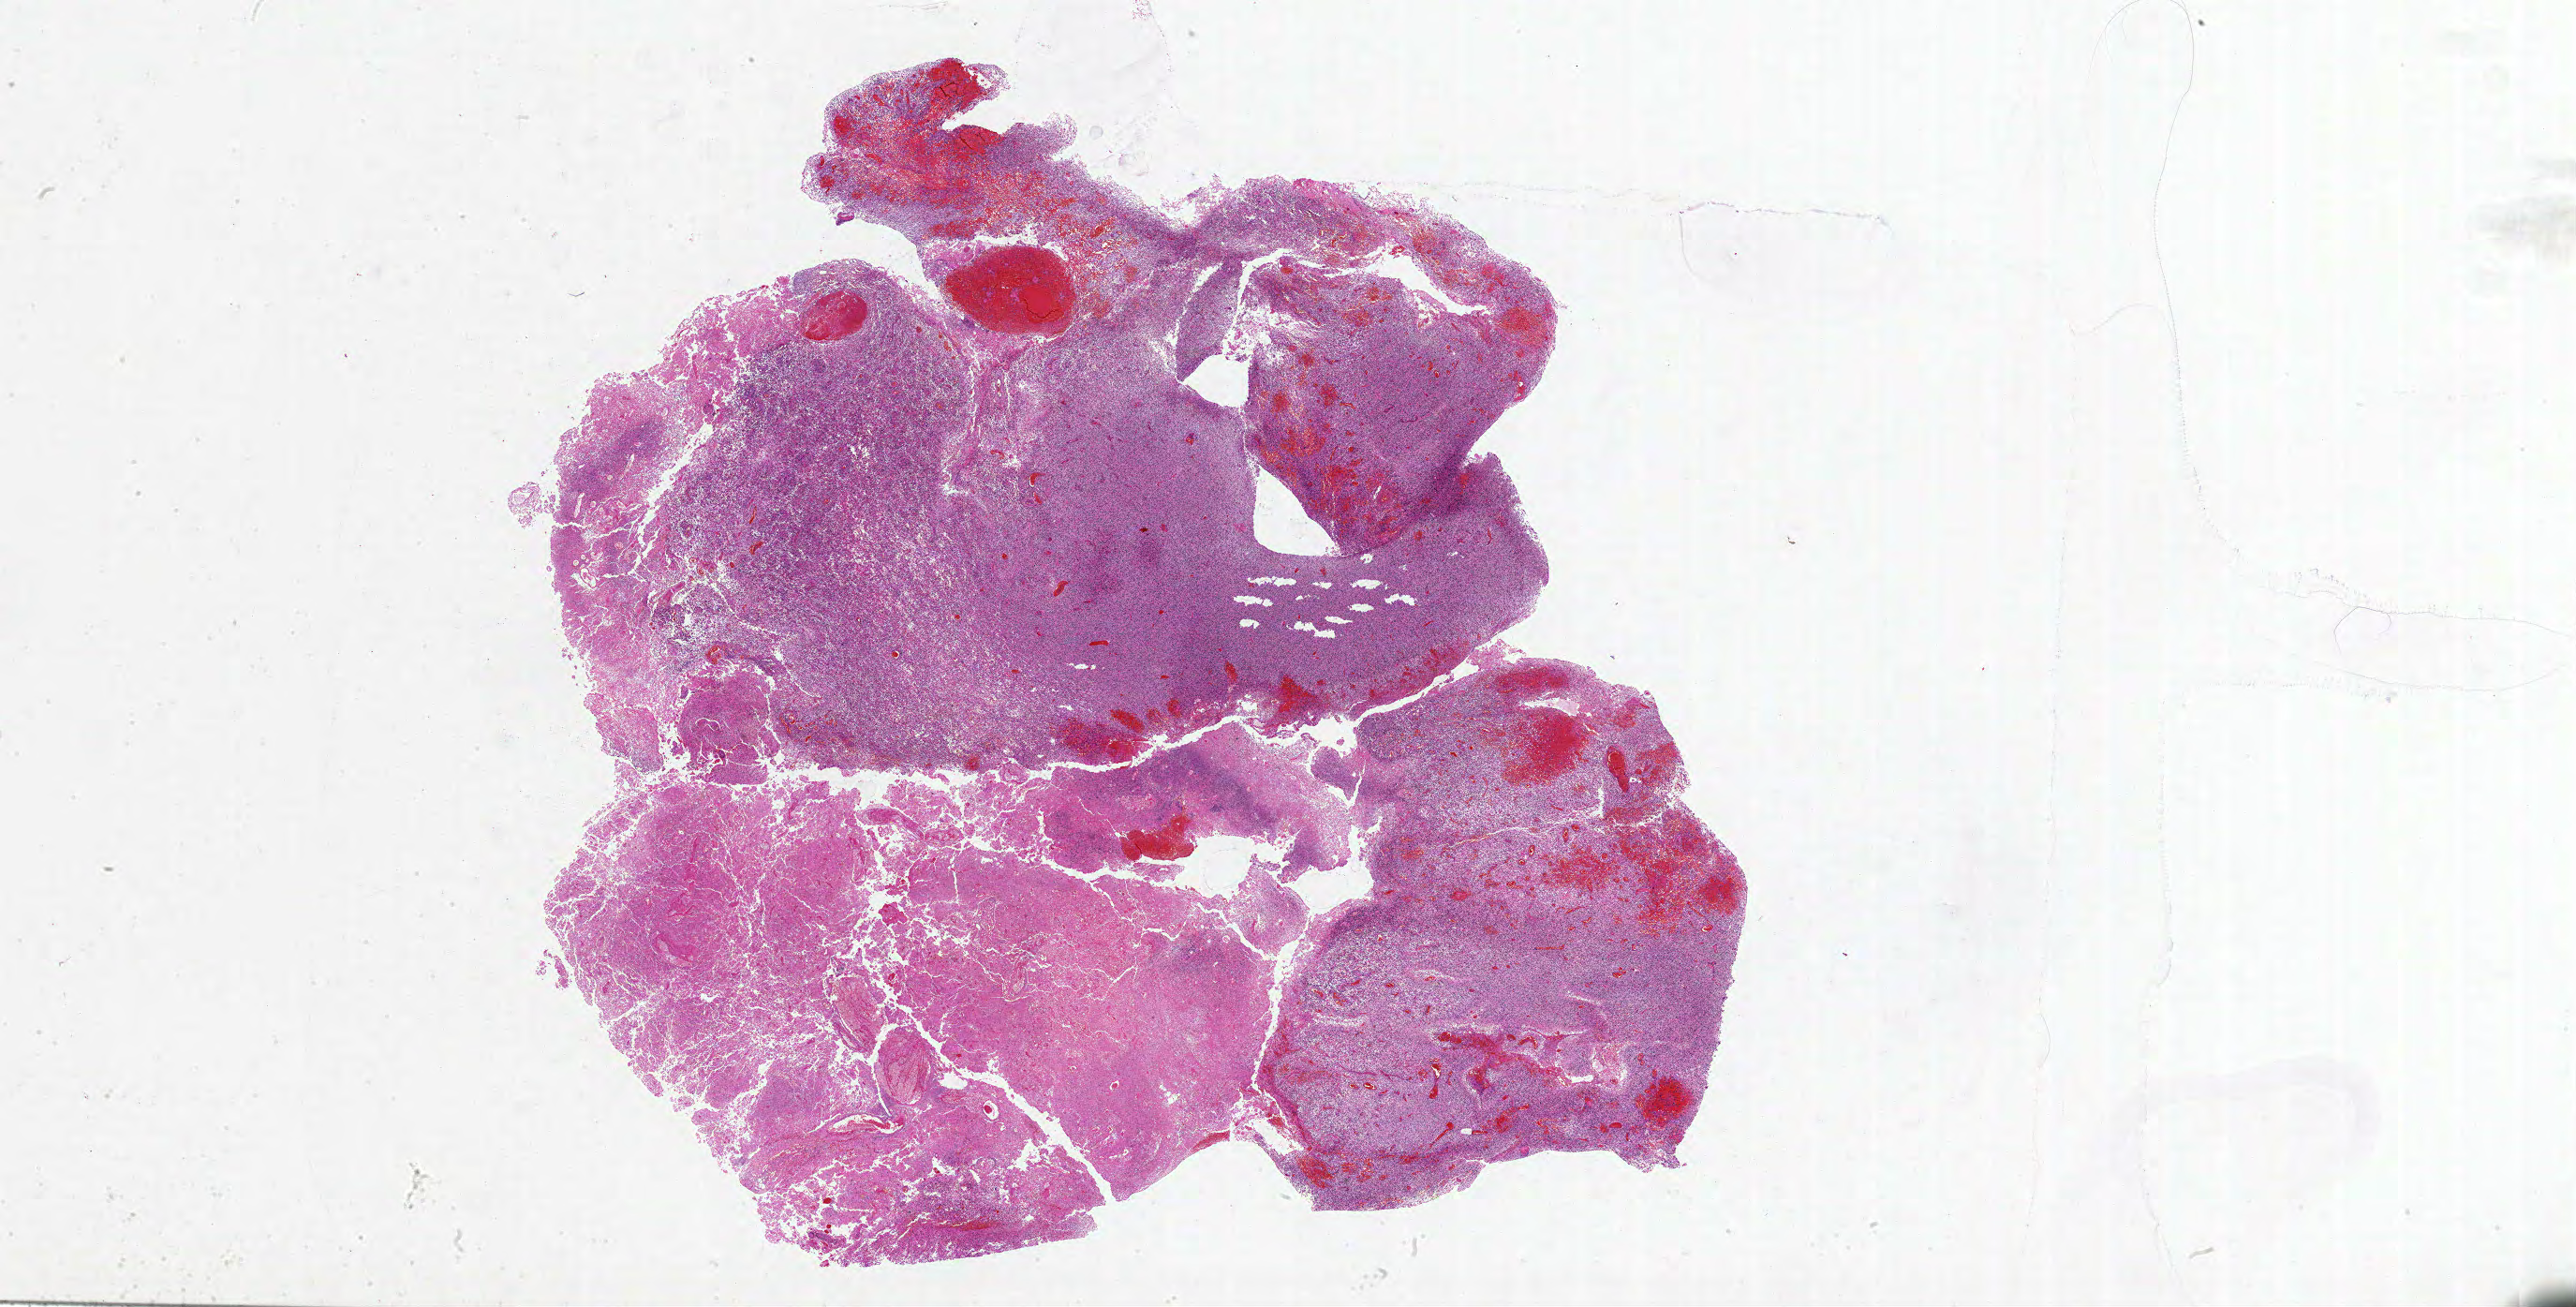
Hematoxylin and eosin (H&E) stained whole-slide image, a low-resolution overview of the entire scanned area, about 44.0 x 22.3 mm; FFPE section; sample: primary tumour, brain. Patient: male, age at initial diagnosis 55 years.
* pathologic diagnosis: Glioblastoma